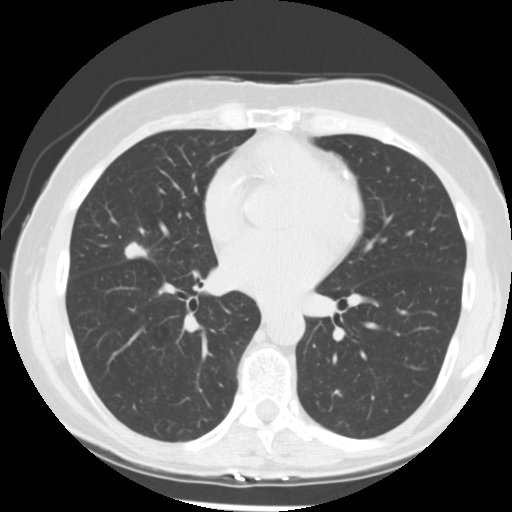
Axial slice from a low-dose chest CT screening exam. First (baseline) screen. Lung window (W 1500 / L -600 HU). 2.5 mm slice thickness. 512 × 512 image matrix. Female participant, aged 66 years at enrolment. Former smoker at enrolment.
Lesion marked by an expert reader, box from (x=118, y=231) to (x=166, y=267) px. The exam's reader record, not a measurement of the box and not confirmed to be the same lesion: non-calcified nodule or mass ≥4 mm, right middle lobe, 15 × 13 mm, poorly defined margins, soft tissue attenuation. Official screen result: positive, change unspecified: nodule(s) >= 4 mm or enlarging nodule(s), mass(es), or other non-specific abnormalities suspicious for lung cancer. Later outcome: lung cancer diagnosed 27 days after this screen — adenocarcinoma, NOS, right middle lobe, undifferentiated (G4), stage IIIA (AJCC 6th edition), 18 mm at pathology.